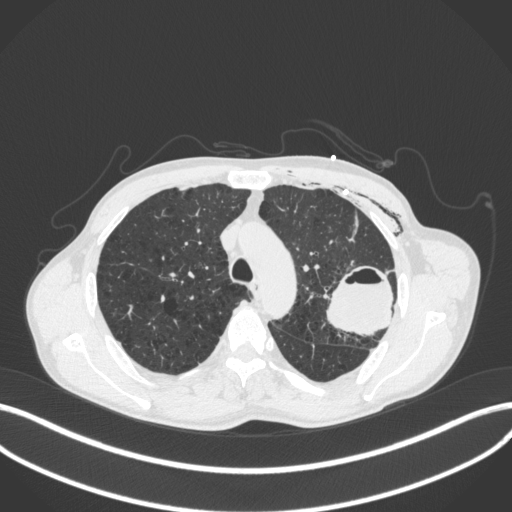
Chest CT, one axial slice. Position 296 of 416 along the scan axis. Reconstruction kernel B31f. Lung window (W 1500 / L -600 HU). 1 mm slice thickness. 512 × 512 image matrix. Patient: male, 58 years. Case-level facts recorded for this patient, not image findings: clinical TNM (as recorded): T3 N0 M0.
Structures marked on this image (bounding box drawn by a radiologist):
- lung tumour (recorded histology: adenocarcinoma): box from (x=328, y=261) to (x=402, y=339) px